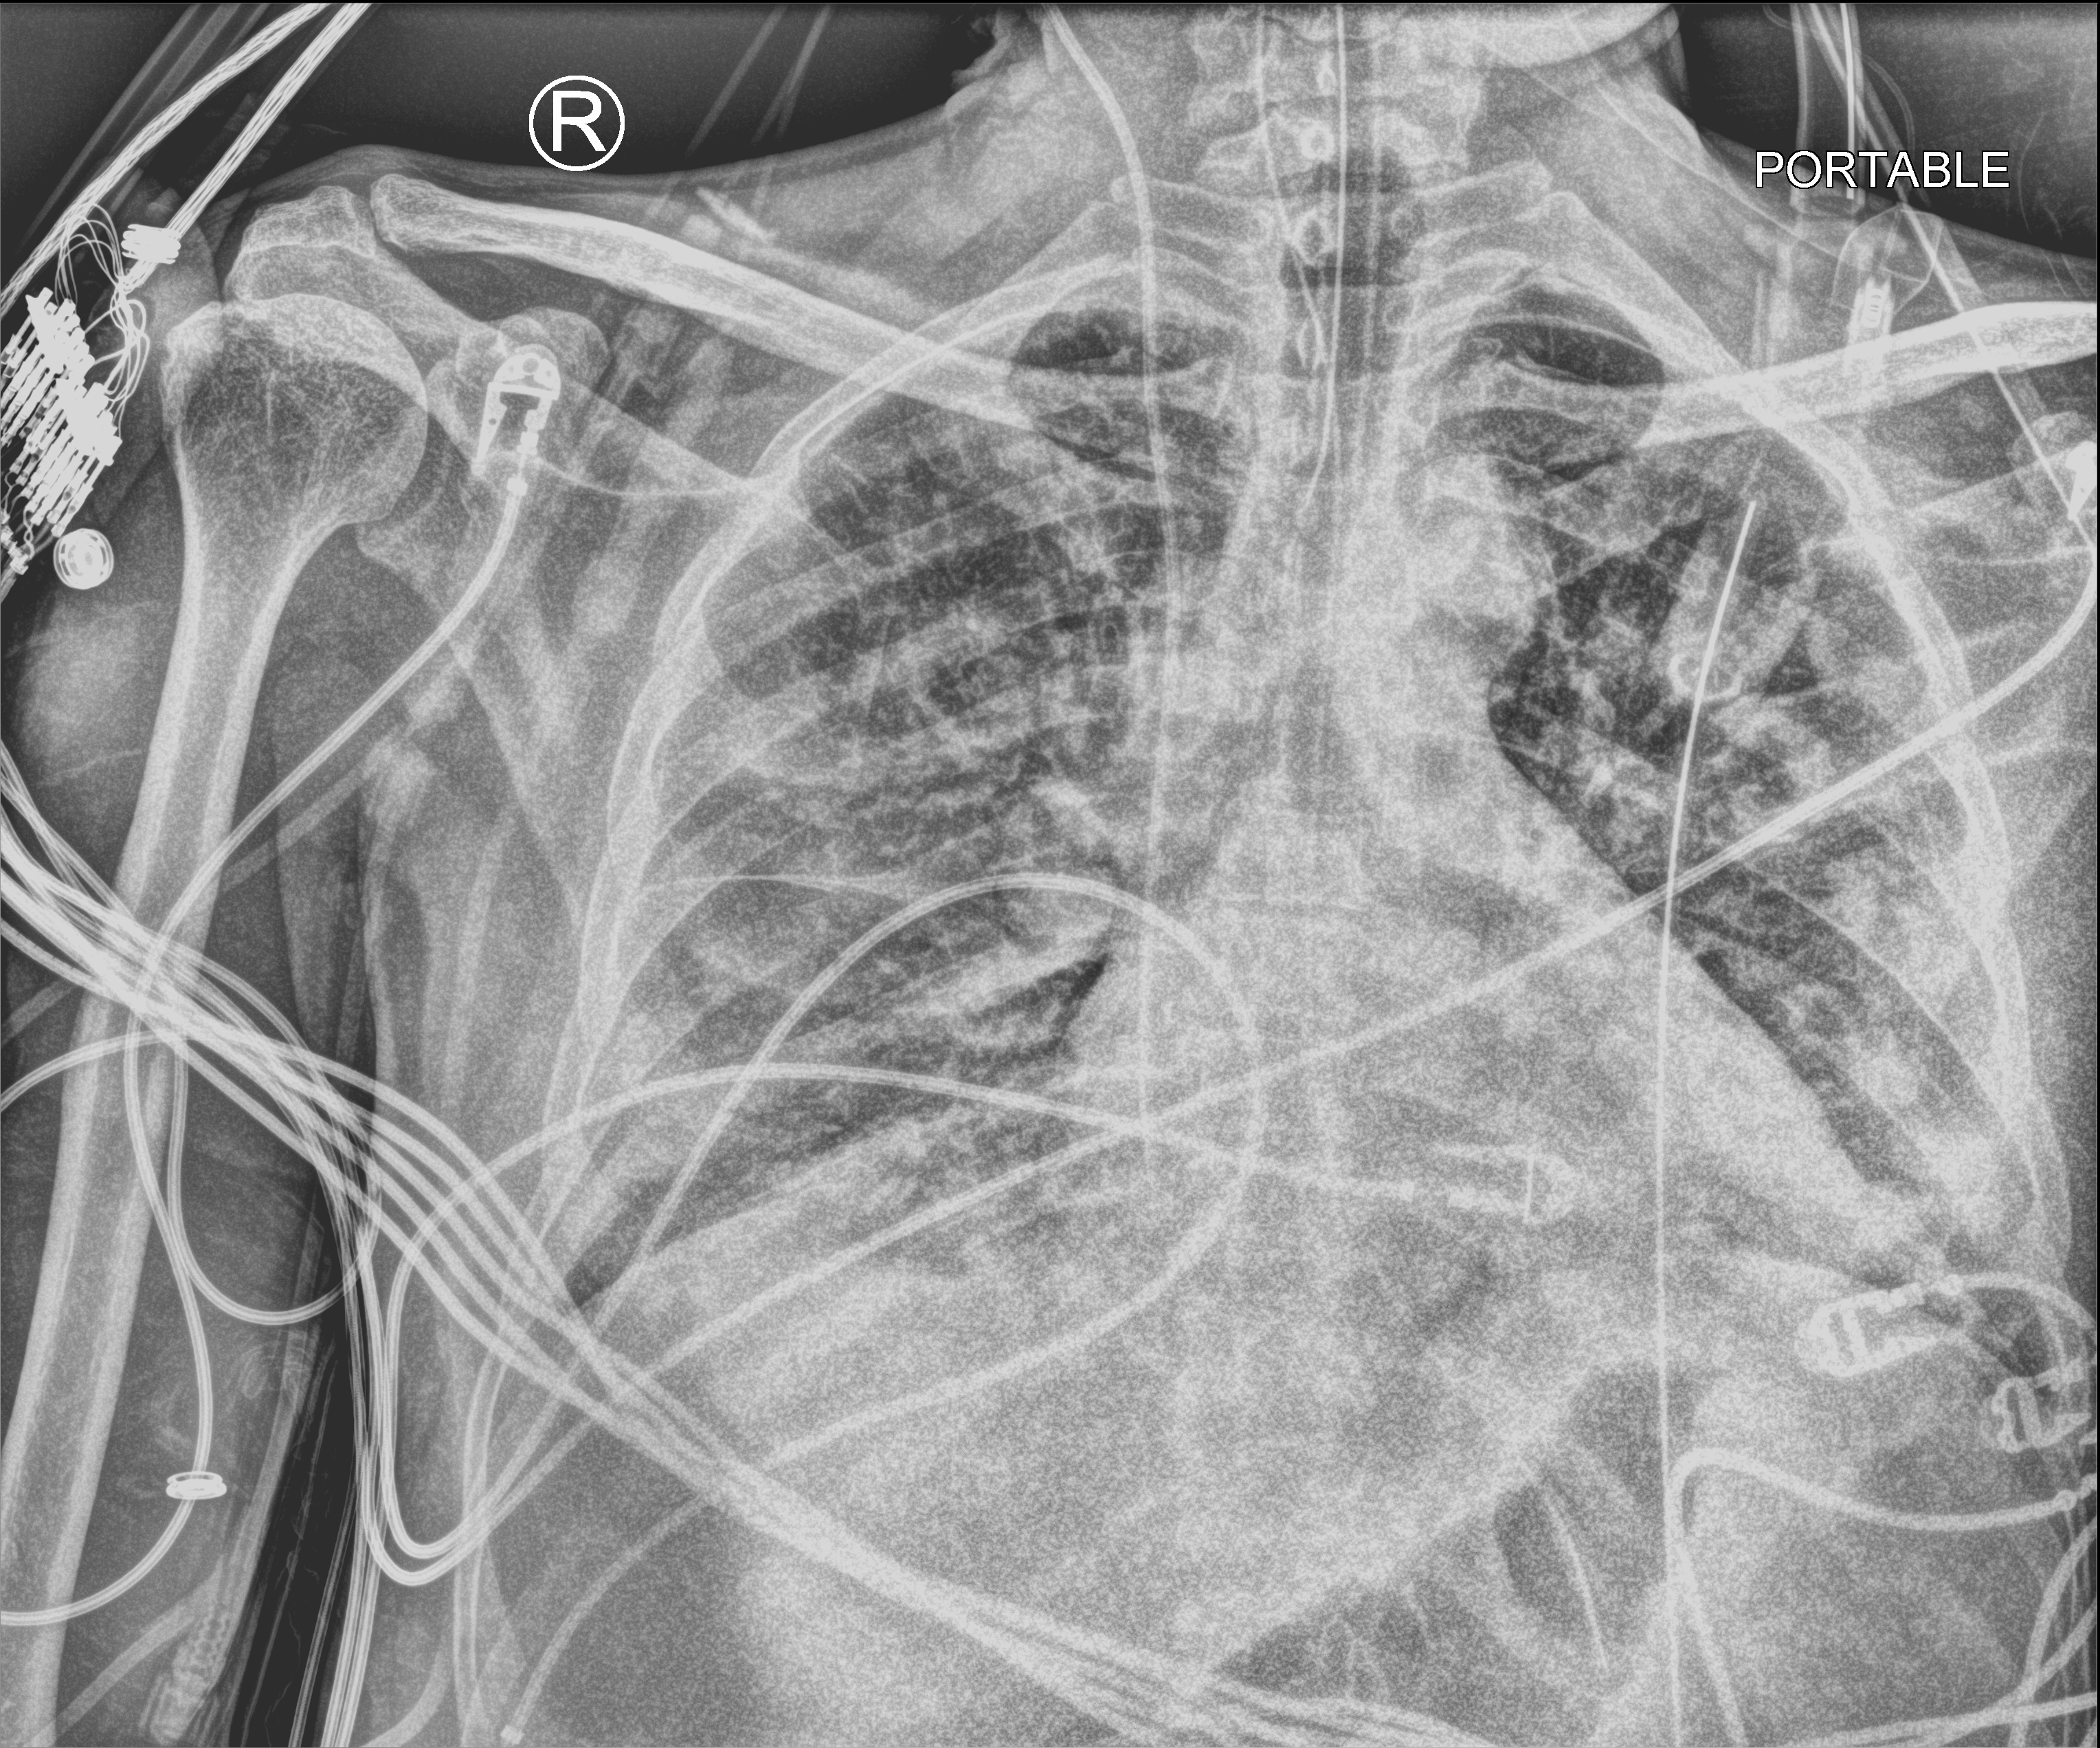
Chest X-ray (portable), anteroposterior (AP) projection. Patient hospitalised with COVID-19; male, aged 18–59 years.
Hospital-stay facts (about this admission, not read from this image; timing relative to this image not recorded): admitted to intensive care during this hospital stay: yes; mechanically ventilated during this hospital stay: yes.